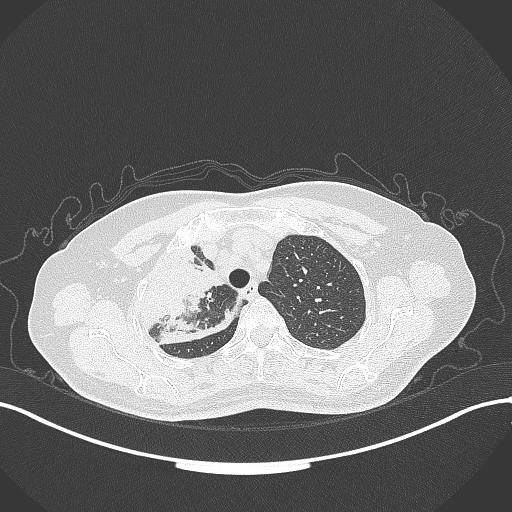
Chest CT, one axial slice. Slice 254 of 309 in the series (ordered by position). Reconstruction kernel B70f. 120 kVp. Lung window (W 1500 / L -600 HU). 1 mm slice thickness. 512 × 512 image matrix, field of view 400 × 400 mm. Female patient, age 60 years. Case-level facts recorded for this patient, not image findings: clinical TNM (as recorded): T3 N1 M1.
Outlined on this slice (bounding box drawn by a radiologist):
- lung tumour (recorded histology: adenocarcinoma): box from (x=121, y=242) to (x=241, y=346) px